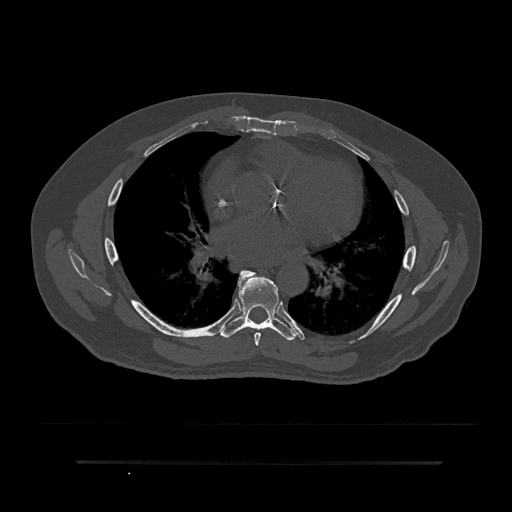
CT including the spine, one axial slice. Slice 495 of 797 in the series (ordered by position). Reconstruction kernel Br40s/3. 120 kVp. Bone window (W 1800 / L 400 HU). 0.5 mm slice thickness. 512 × 512 image matrix, field of view 464 × 464 mm. Patient: male, 59 years. From the clinical record (not read from this slice): primary cancer: bile ducts; vertebrae with lytic lesions (as recorded): T10.
Annotated regions visible in this slice (semi-automatic segmentation, software-assisted and operator-edited):
- T6 vertebra: bounding box [x1, y1, x2, y2] px = [238, 273, 261, 346]
- T7 vertebra: [220, 270, 296, 341]